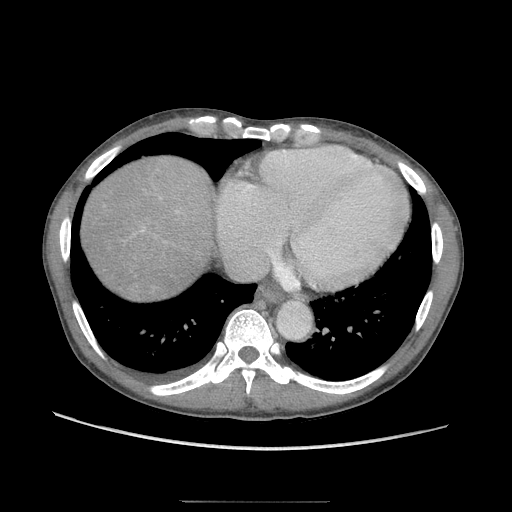
Contrast-enhanced abdominal CT (liver protocol), one axial slice. Slice 92 of 103 in the series (ordered by position). 120 kVp. Soft-tissue window (W 400 / L 40 HU). 2.5 mm slice thickness. 512 × 512 image matrix. Case-level facts recorded for this patient, not image findings: diagnosis: hepatocellular carcinoma (patient treated with transarterial chemoembolisation; whether this scan precedes or follows treatment is not stated here); TNM stage (as recorded): Stage-IIIA; Child-Pugh class: A; tumour differentiation: moderately differentiated.
Structures marked on this image (semi-automatically segmented with operator editing):
- abdominal aorta: bounding box (x1, y1, x2, y2) in pixels: (277, 301, 310, 338)
- liver parenchyma outside the tumour (the mass and vessels are separate outlines, so this box may not span the whole liver): (84, 156, 210, 290)